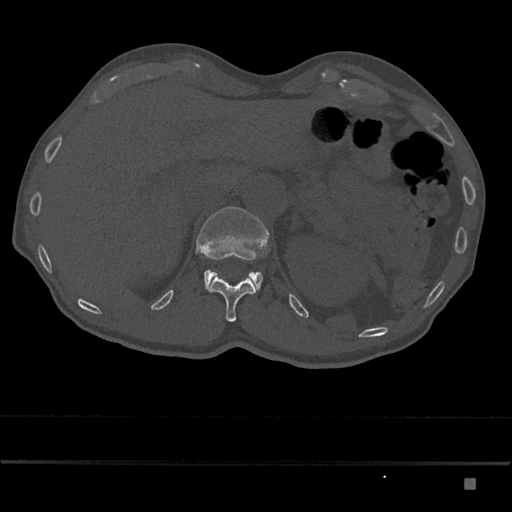
CT including the spine, one axial slice; slice 585 of 797 in the series (ordered by position); 120 kVp; bone window (W 1800 / L 400 HU); 0.5 mm slice thickness; 512 × 512 image matrix, field of view 390 × 390 mm. Male patient, age 72 years. Case-level facts recorded for this patient, not image findings: primary cancer: prostate.
Annotated regions visible in this slice (semi-automatically segmented with operator editing):
- L1 vertebra: bounding box <196,207,269,293> (left, top, right, bottom; pixels)
- T12 vertebra: <206,276,256,322>